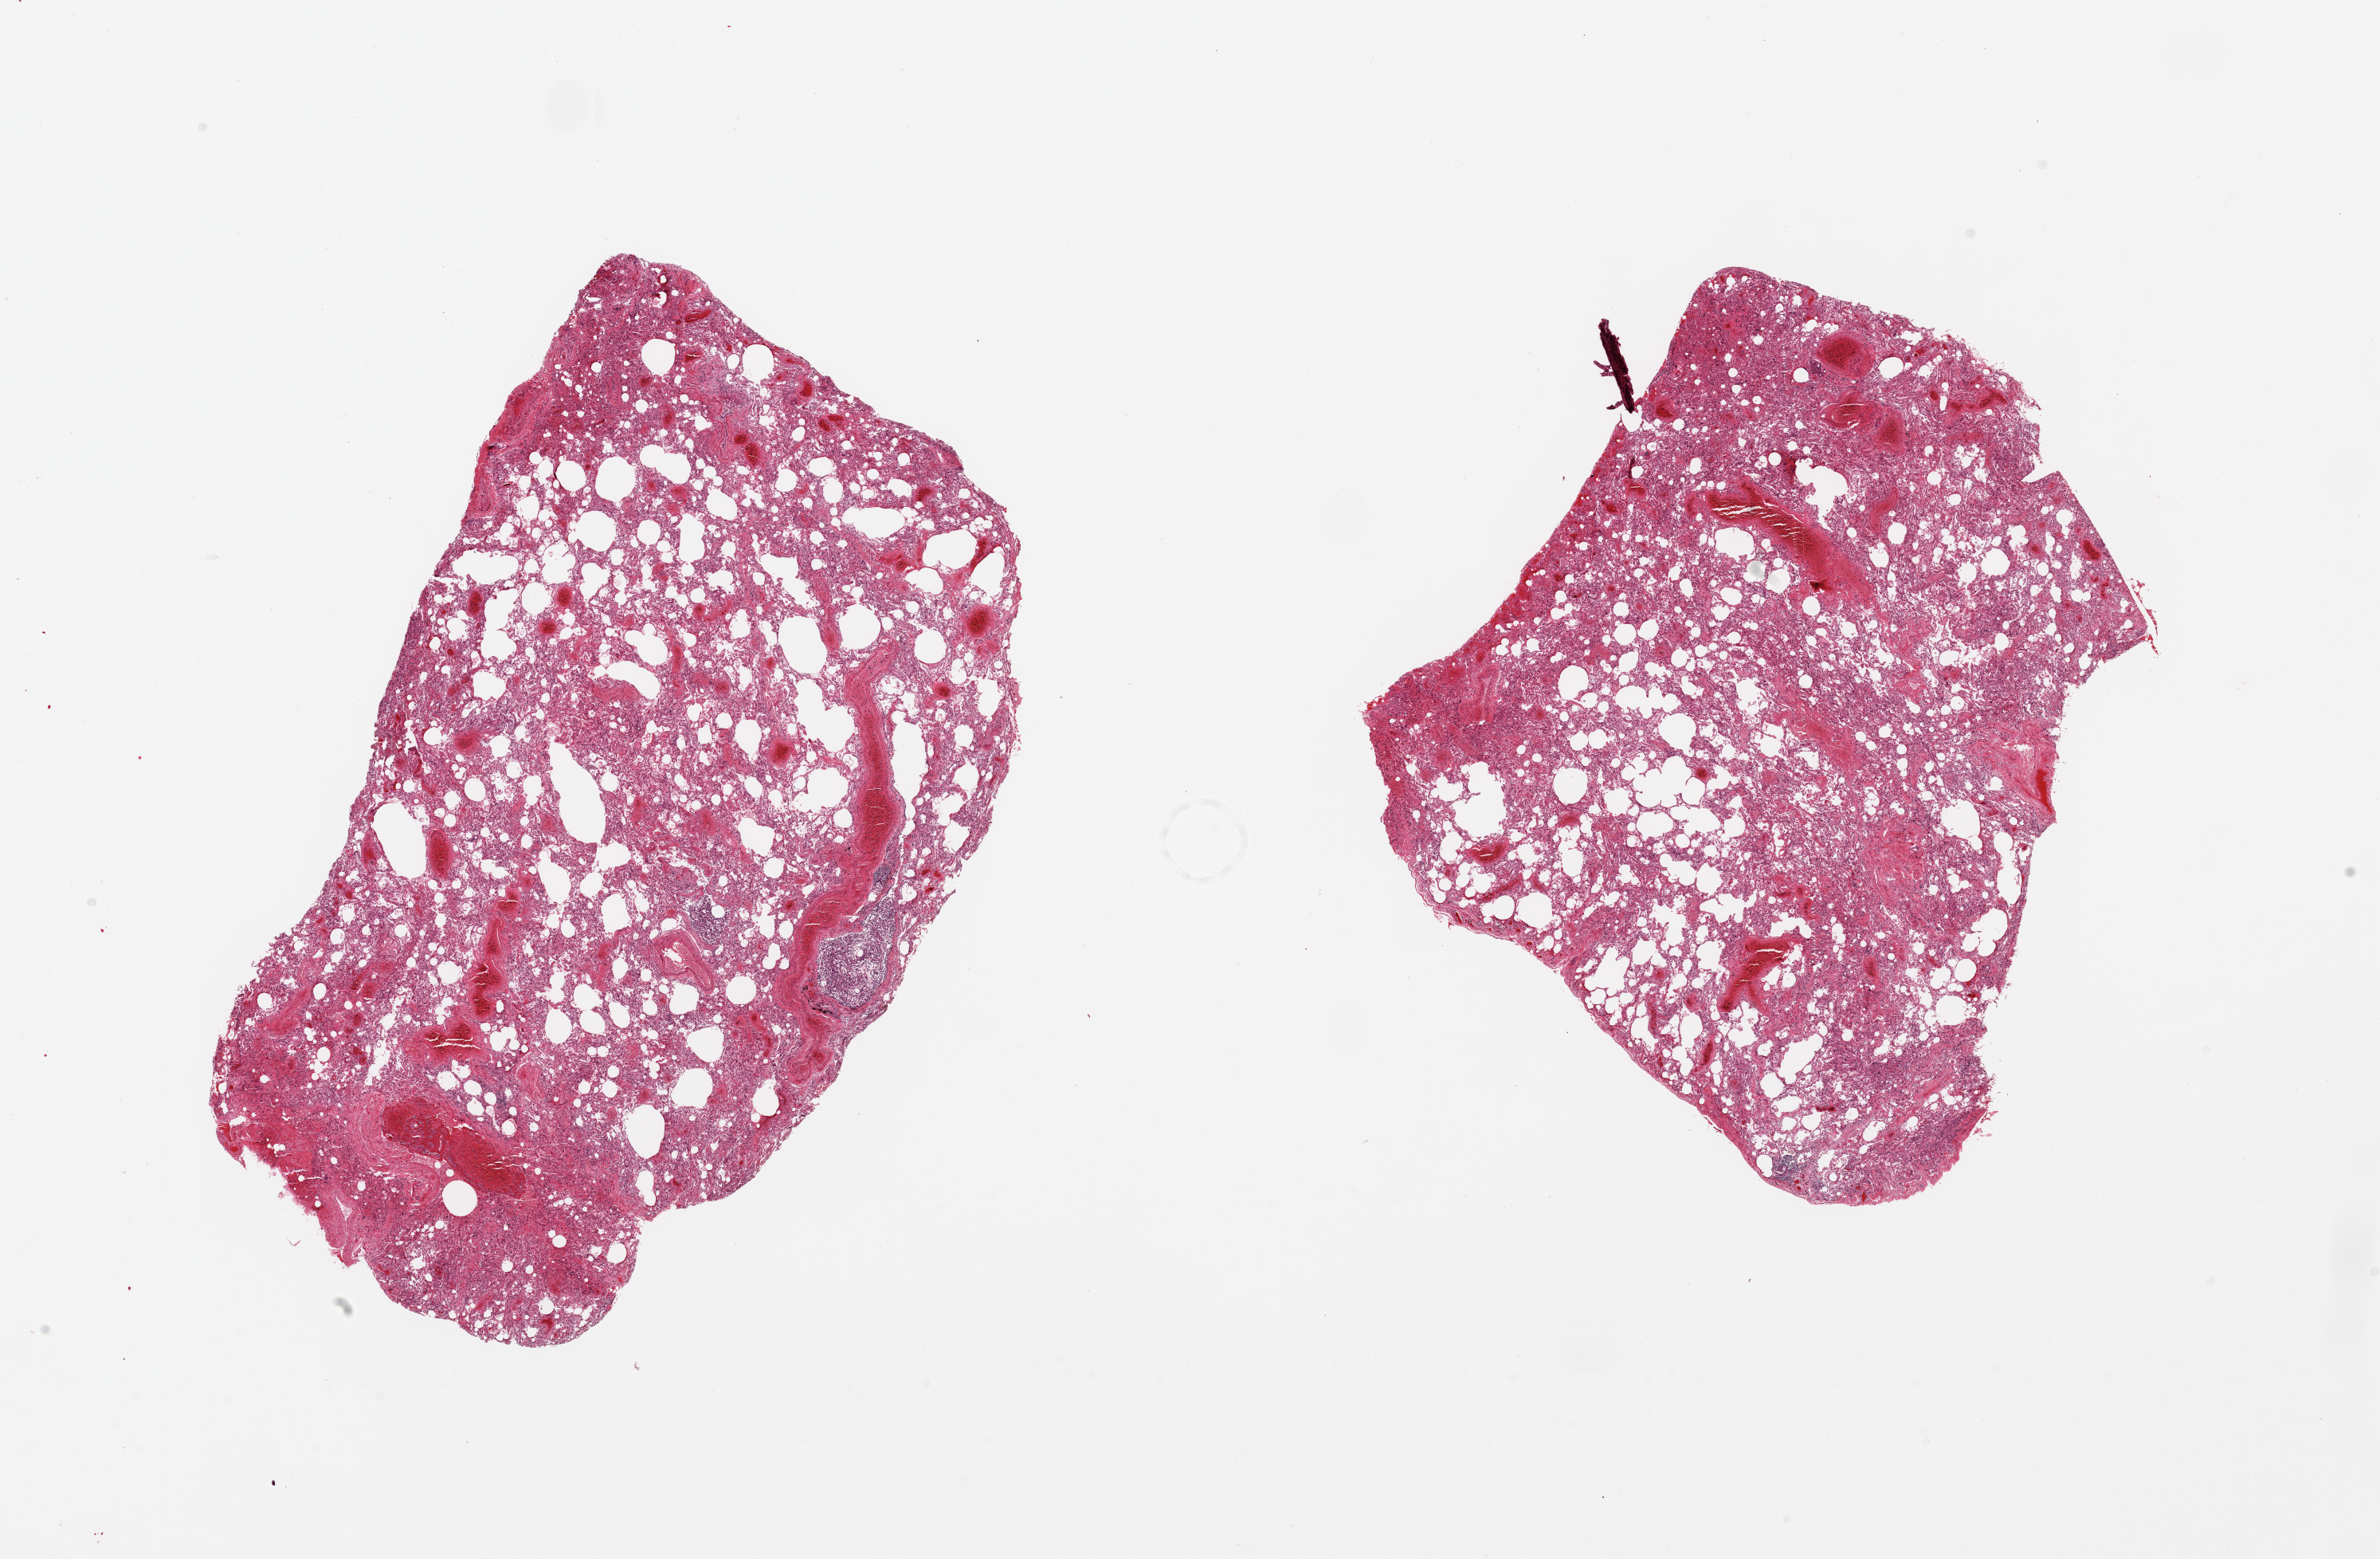
Digitized hematoxylin and eosin (H&E)-stained section, brightfield, low-resolution overview of the scanned area, about 23.6 x 15.5 mm (slide scanned at 20x). PAXgene-fixed paraffin-embedded (PFPE) section. Target tissue: lung. Tissue donor sample. Female donor.
• pathologist's review note for this sample: 2 pieces; congestion and atelectasis, few collections of lymphocytes